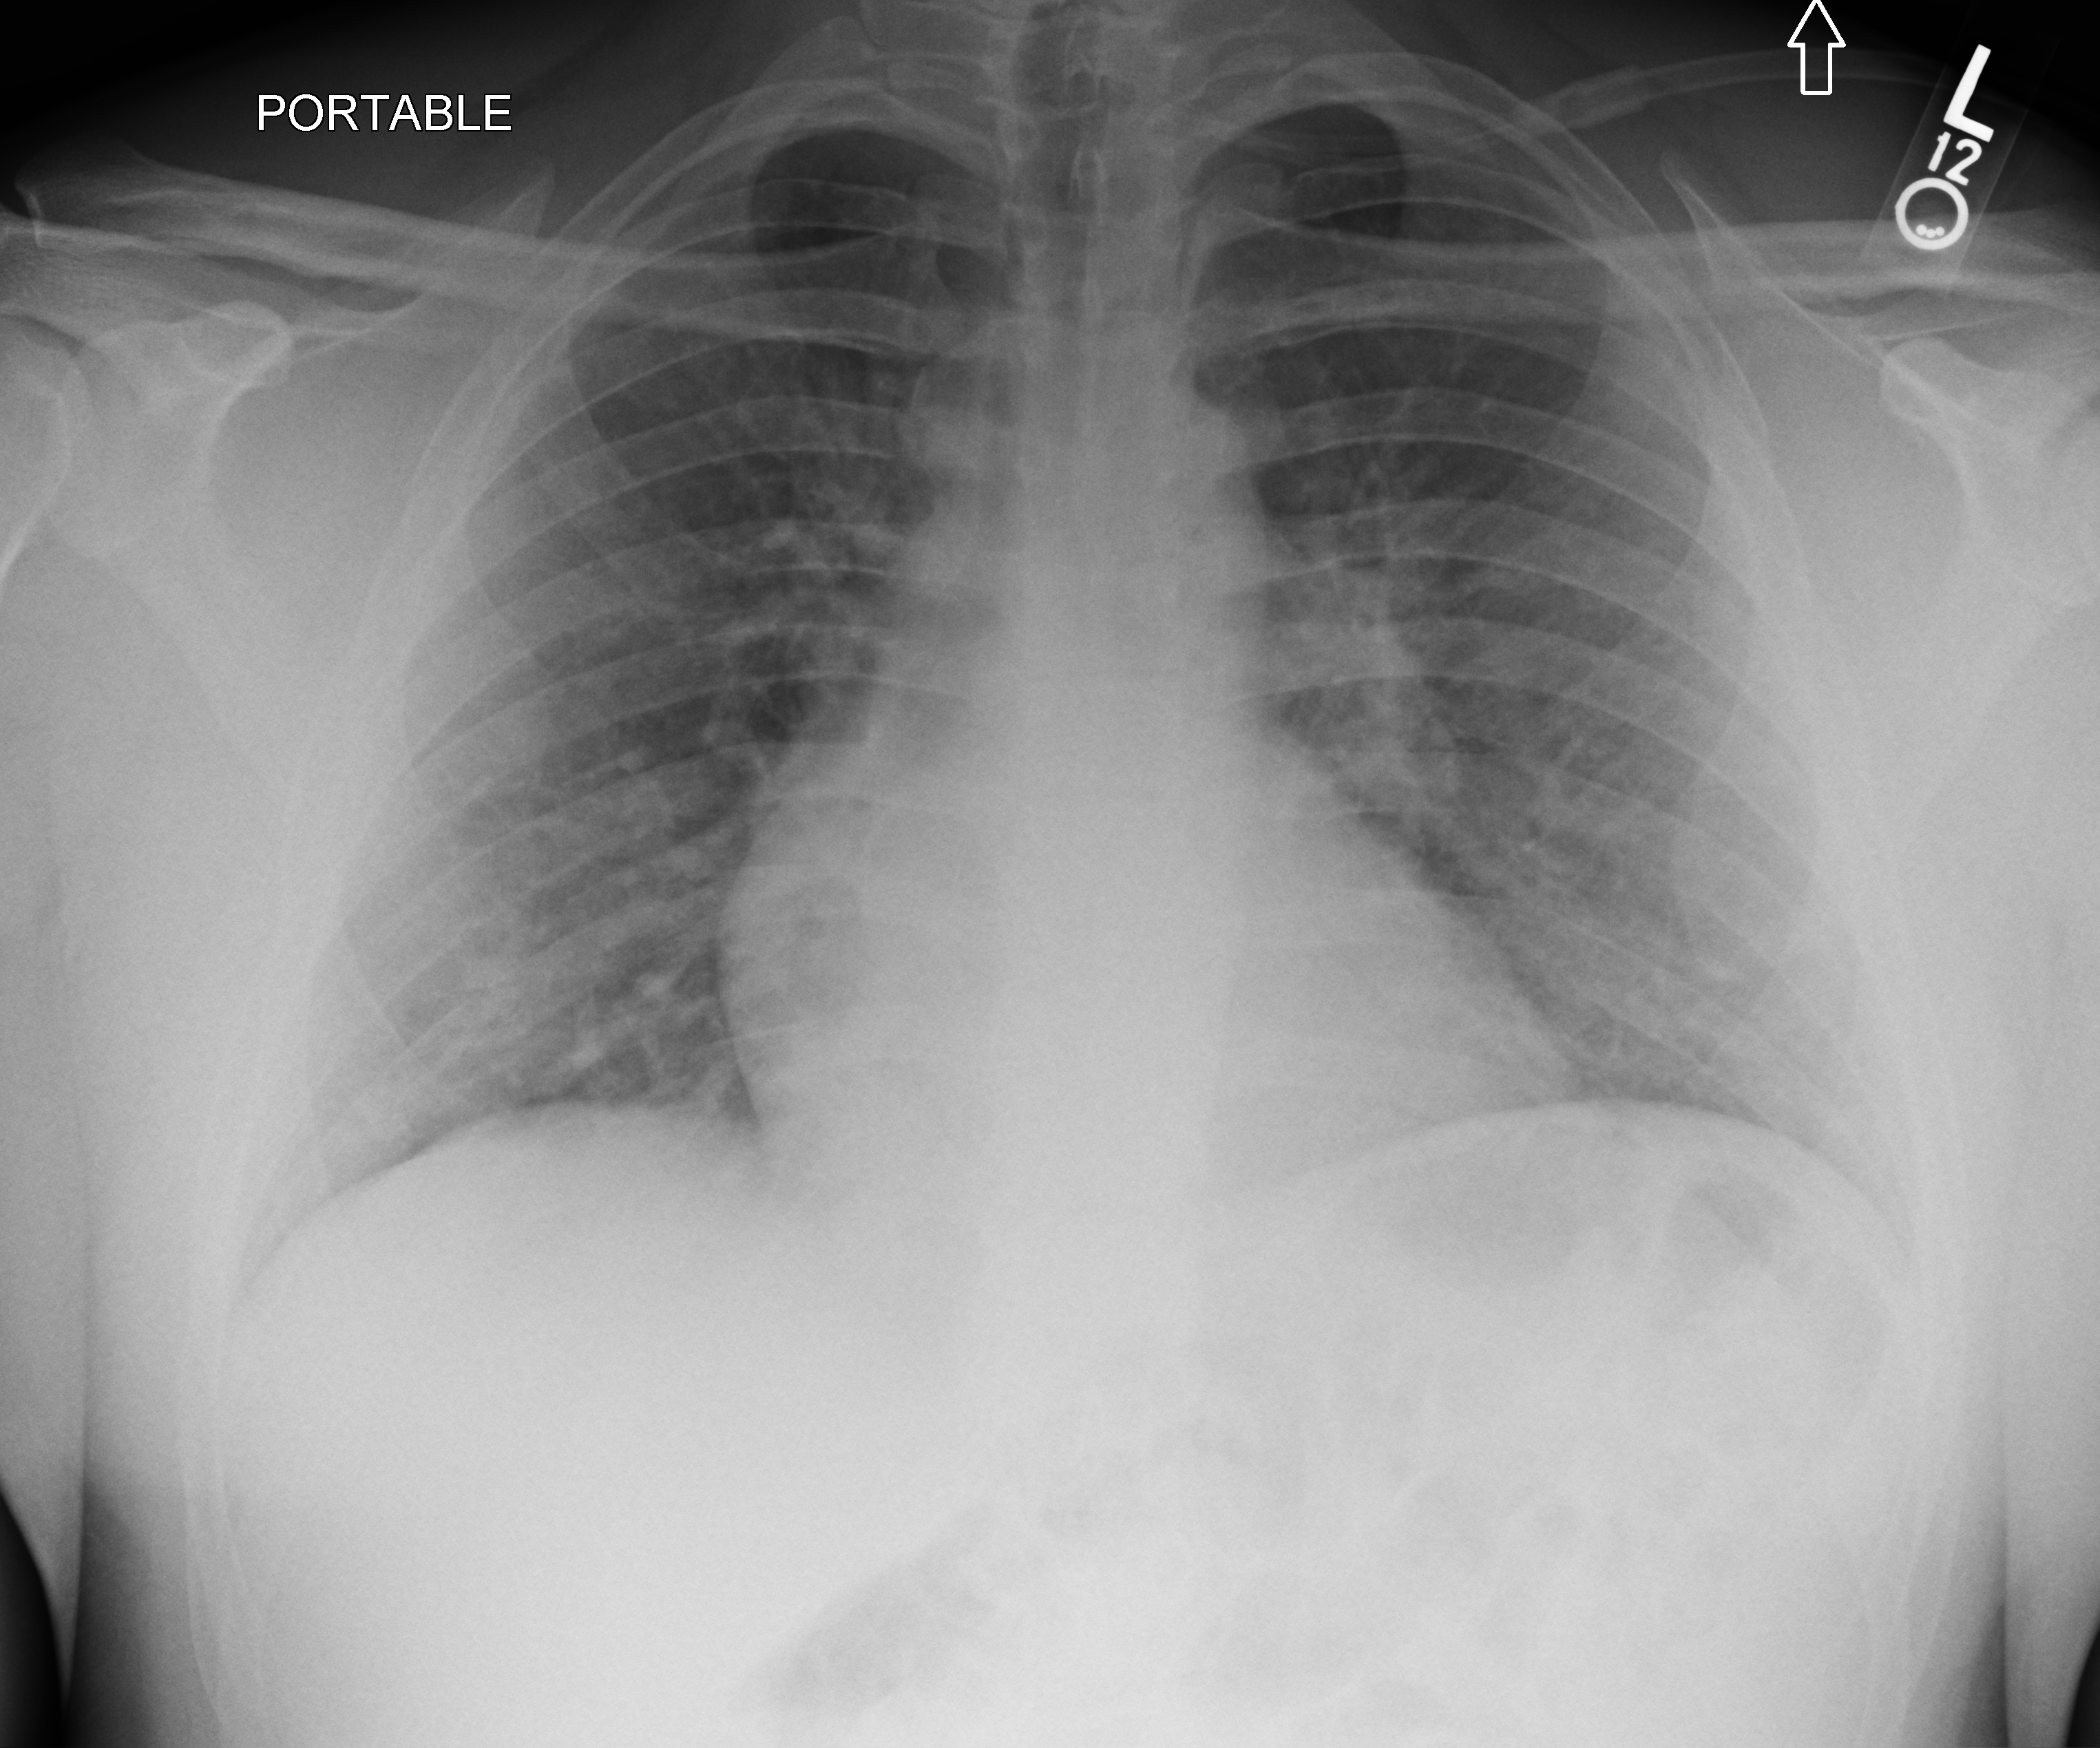
Chest X-ray (portable), anteroposterior (AP) projection. Male patient hospitalised with COVID-19, age 18–59 years.
Admission-level facts for this patient (not findings on this image; timing relative to this image not recorded): admitted to intensive care during this hospital stay: no.